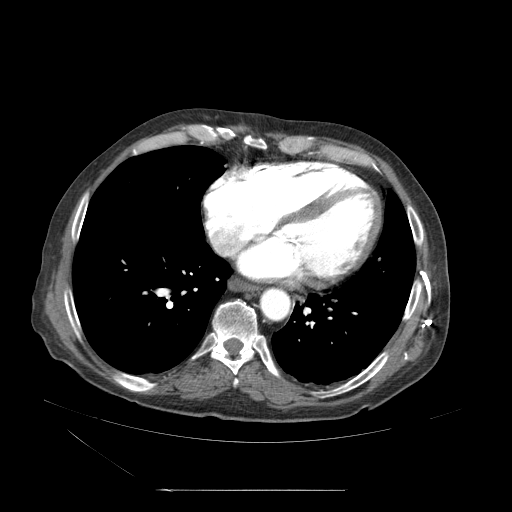
Contrast-enhanced abdominal CT (liver protocol), one axial slice; 120 kVp; soft-tissue window (W 400 / L 40 HU); 2.5 mm slice thickness; 512 × 512 image matrix. From the clinical record (not read from this slice): diagnosis: hepatocellular carcinoma (patient treated with transarterial chemoembolisation; whether this scan precedes or follows treatment is not stated here); TNM stage (as recorded): Stage-II; Child-Pugh class: A; tumour nodularity: multinodular; tumour size: 1 cm.
Structures marked on this image (semi-automatic segmentation, software-assisted and operator-edited):
- abdominal aorta: box from (x=260, y=288) to (x=290, y=320) px